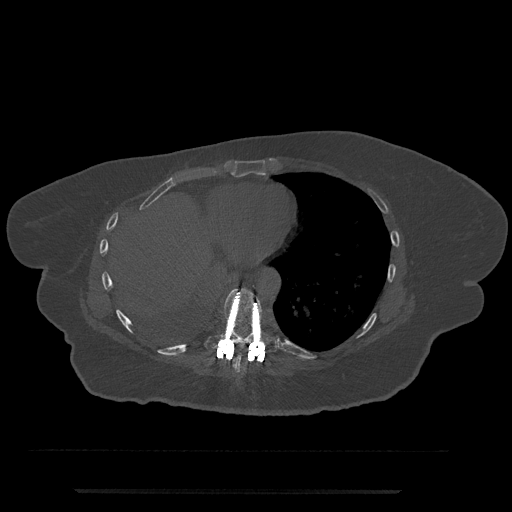
CT including the spine, one axial slice; position 348 of 797 along the scan axis; reconstruction kernel Br40s/3; 120 kVp; bone window (W 1800 / L 400 HU); 512 × 512 image matrix. Patient: female, 51 years. From the clinical record (not read from this slice): primary cancer: neuro; vertebrae with lytic lesions (as recorded): T8.
Annotated regions visible in this slice (semi-automatically segmented with operator editing):
- T8 vertebra: bounding box <233,344,264,374> (left, top, right, bottom; pixels)
- T9 vertebra: <205,288,277,362>